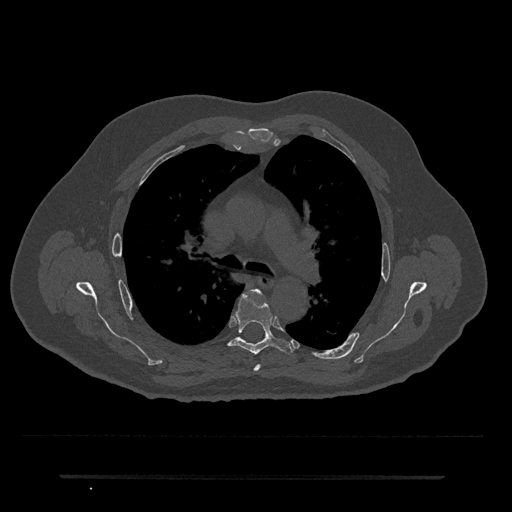
CT including the spine, one axial slice. Slice 487 of 797 in the series (ordered by position). Bone window (W 1800 / L 400 HU). 0.5 mm slice thickness. 512 × 512 image matrix, field of view 437 × 437 mm. Male patient, age 69 years. From the clinical record (not read from this slice): primary cancer: prostate.
Annotated regions visible in this slice (semi-automatic segmentation, software-assisted and operator-edited):
- T4 vertebra: bounding box [x1, y1, x2, y2] px = [252, 289, 261, 372]
- T5 vertebra: [228, 291, 293, 355]